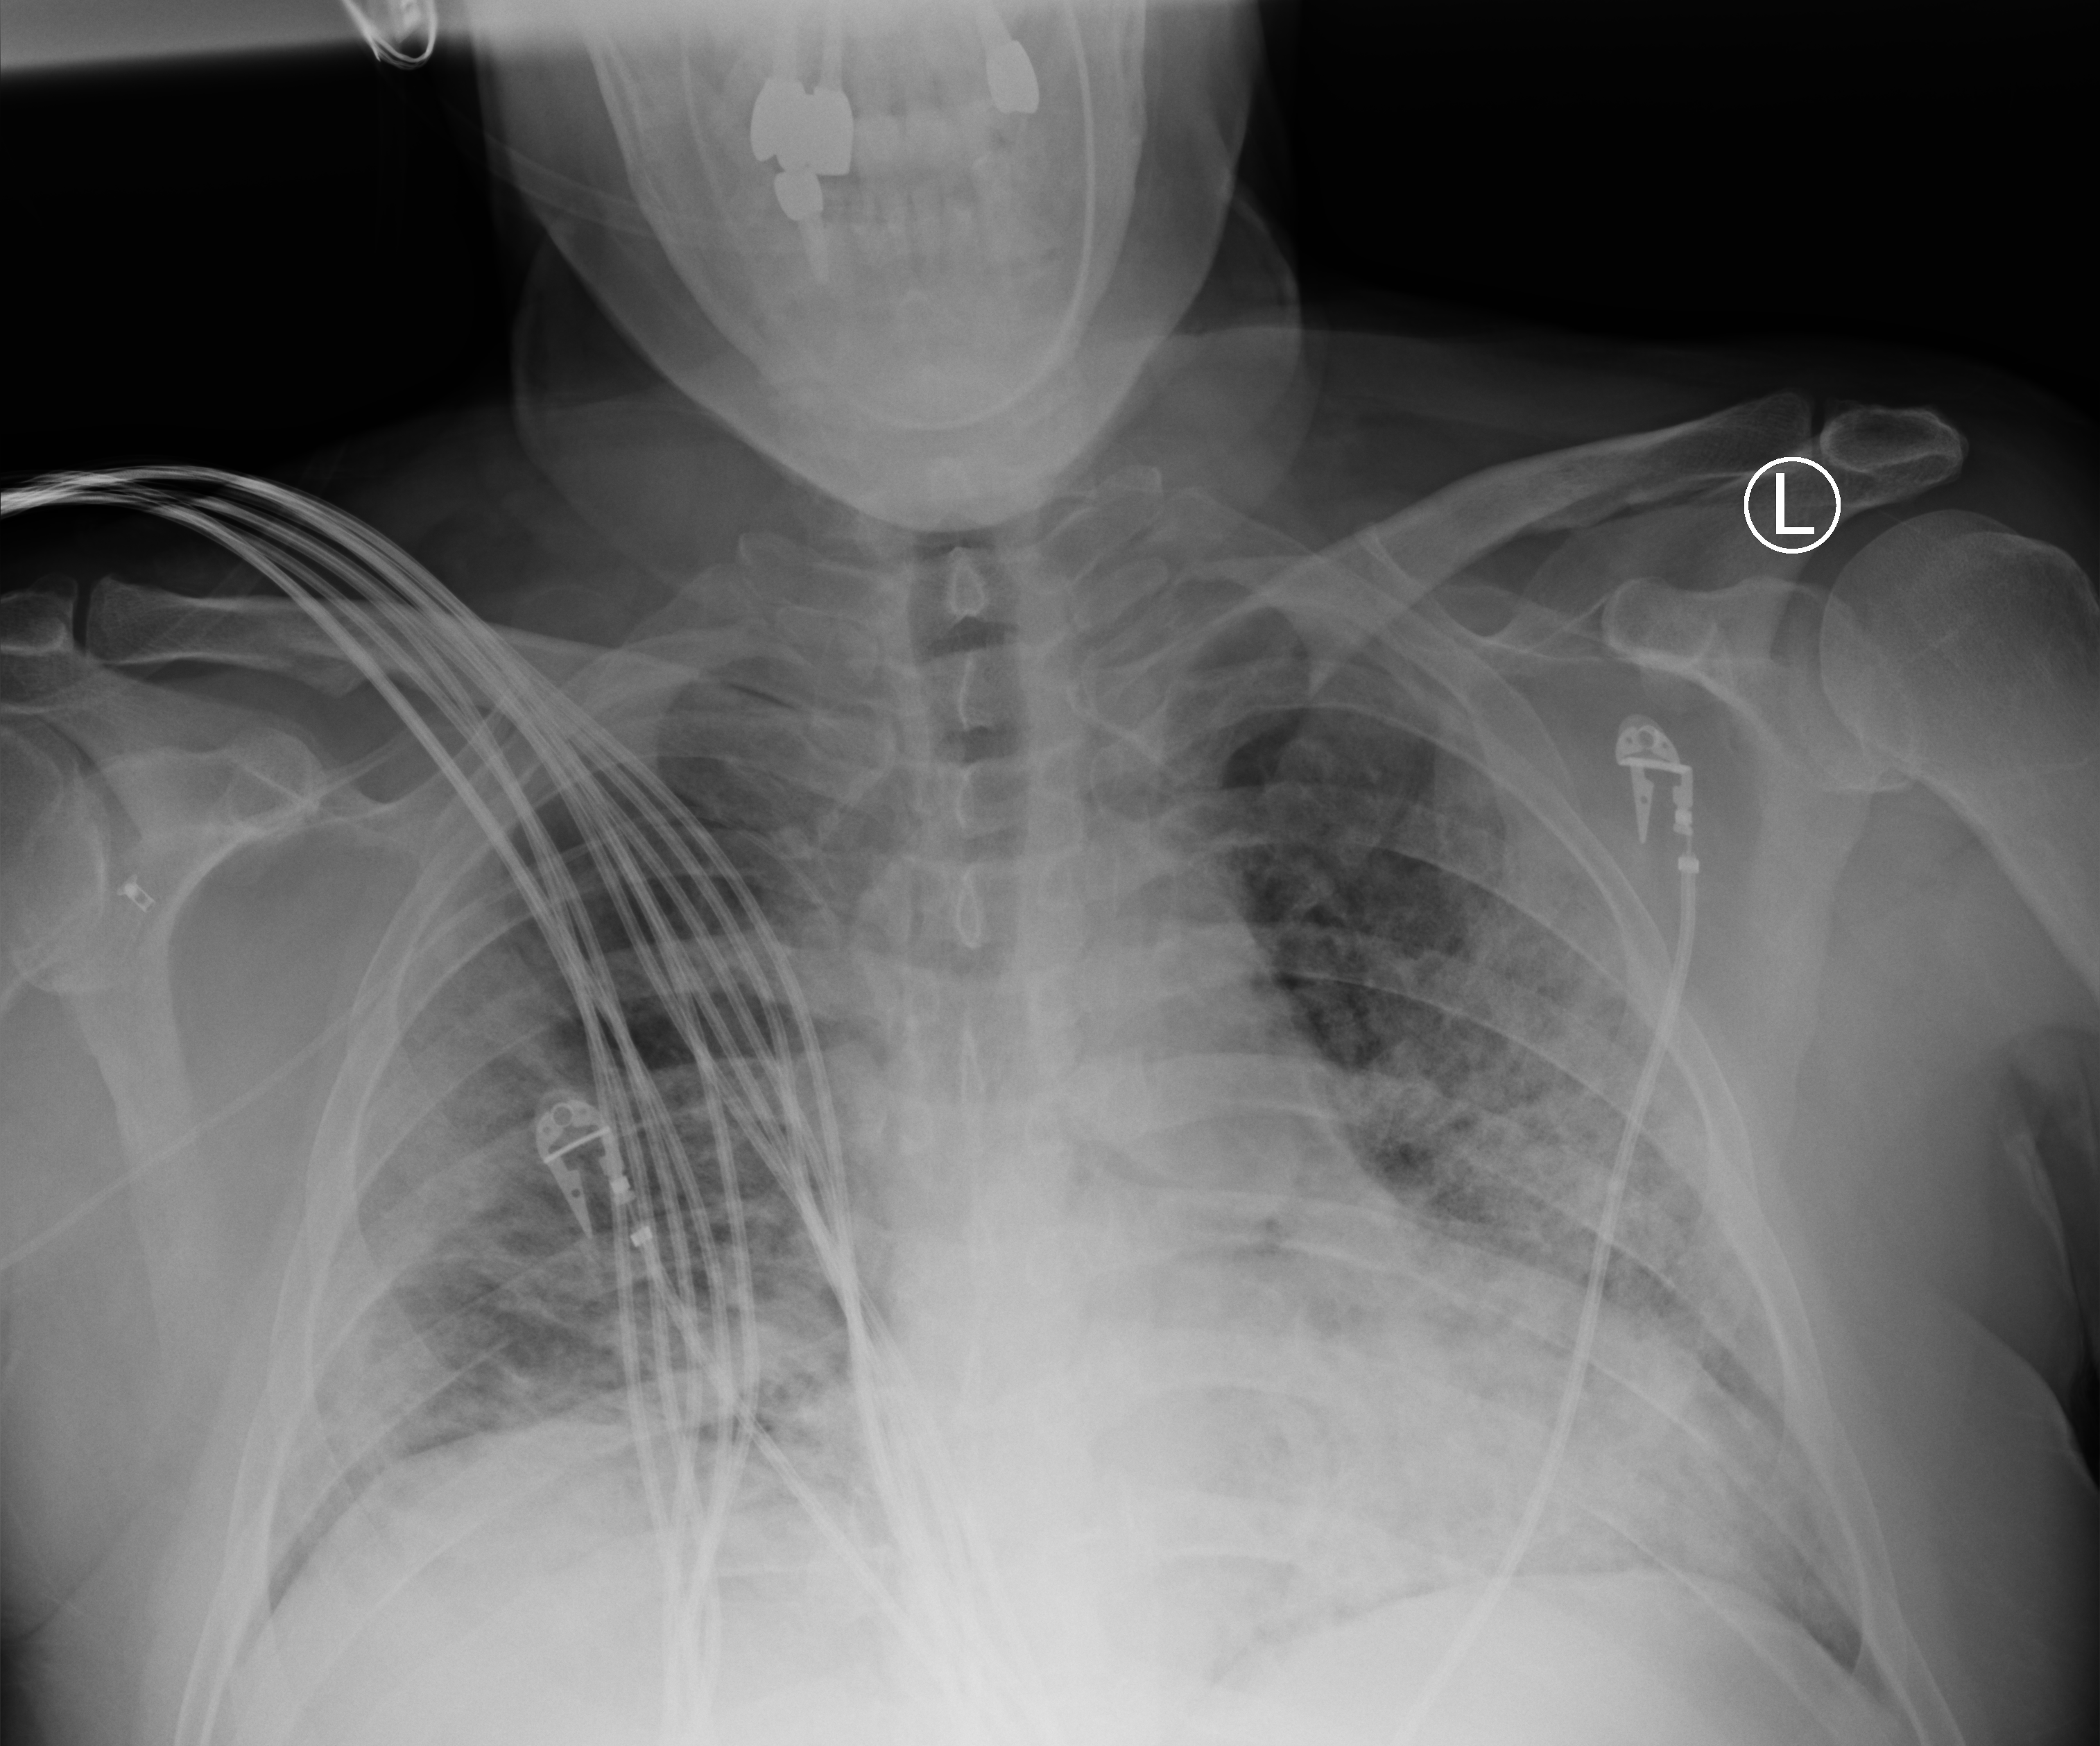
Portable chest radiograph. Patient hospitalised with COVID-19; male, aged 18–59 years.
Hospital-stay facts (about this admission, not read from this image; timing relative to this image not recorded): length of hospital stay: 52 days.